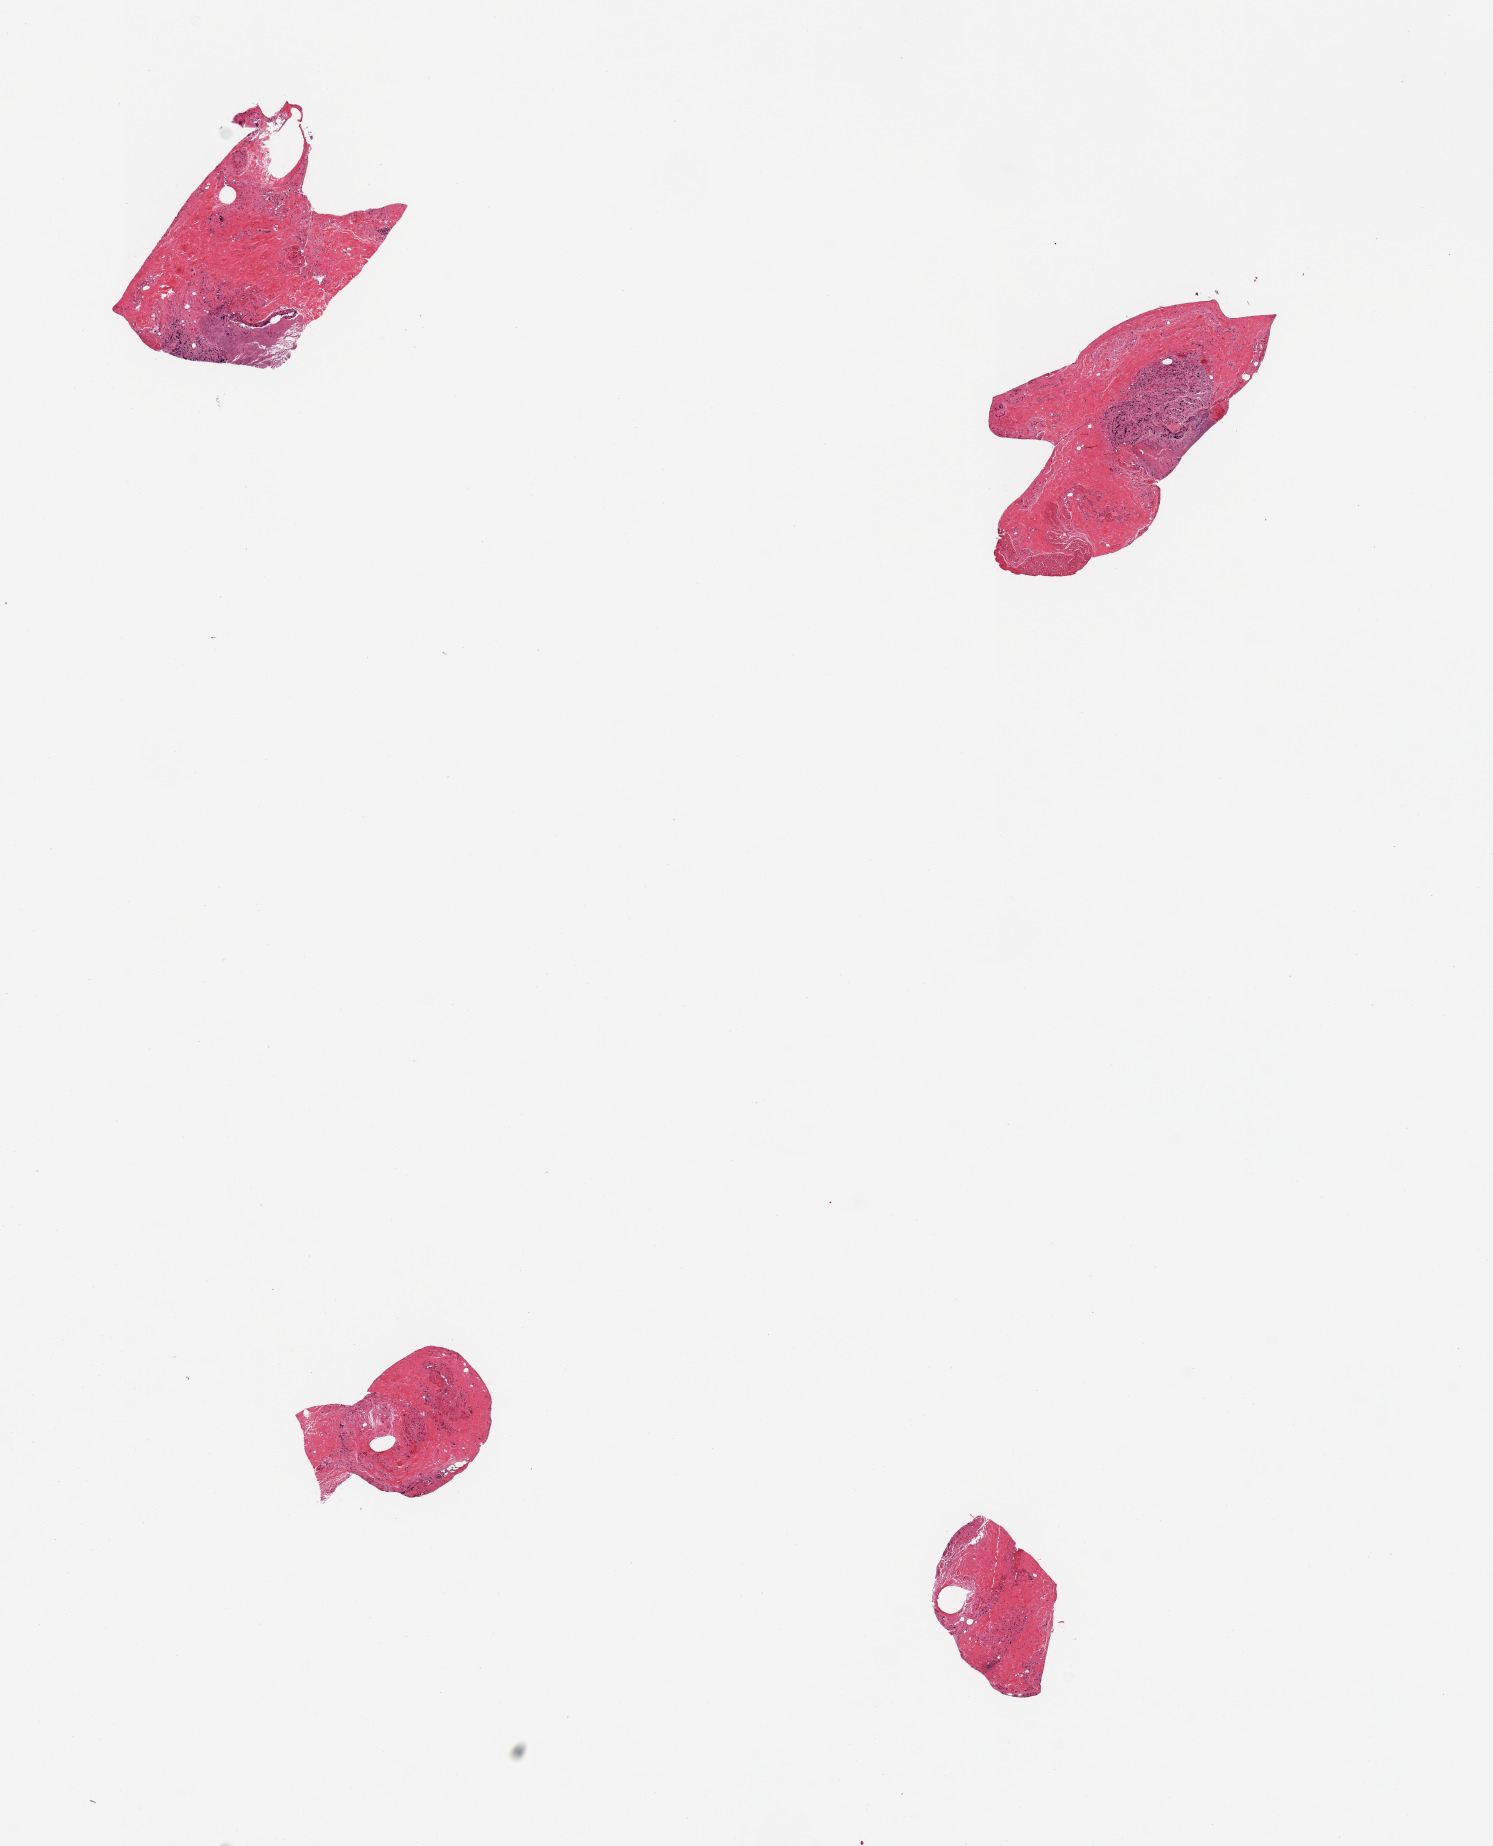
Digitized haematoxylin and eosin-stained section — shown as a low-resolution overview of the whole scanned area (about 11.8 x 14.6 mm). PAXgene-fixed paraffin-embedded (PFPE) section. Section of transverse colon (target tissue). Tissue donor sample. Female donor.
Pathologist's review note for this sample: 4 pieces; variable fragments including autolyzed mucosa and portion of muscularis.